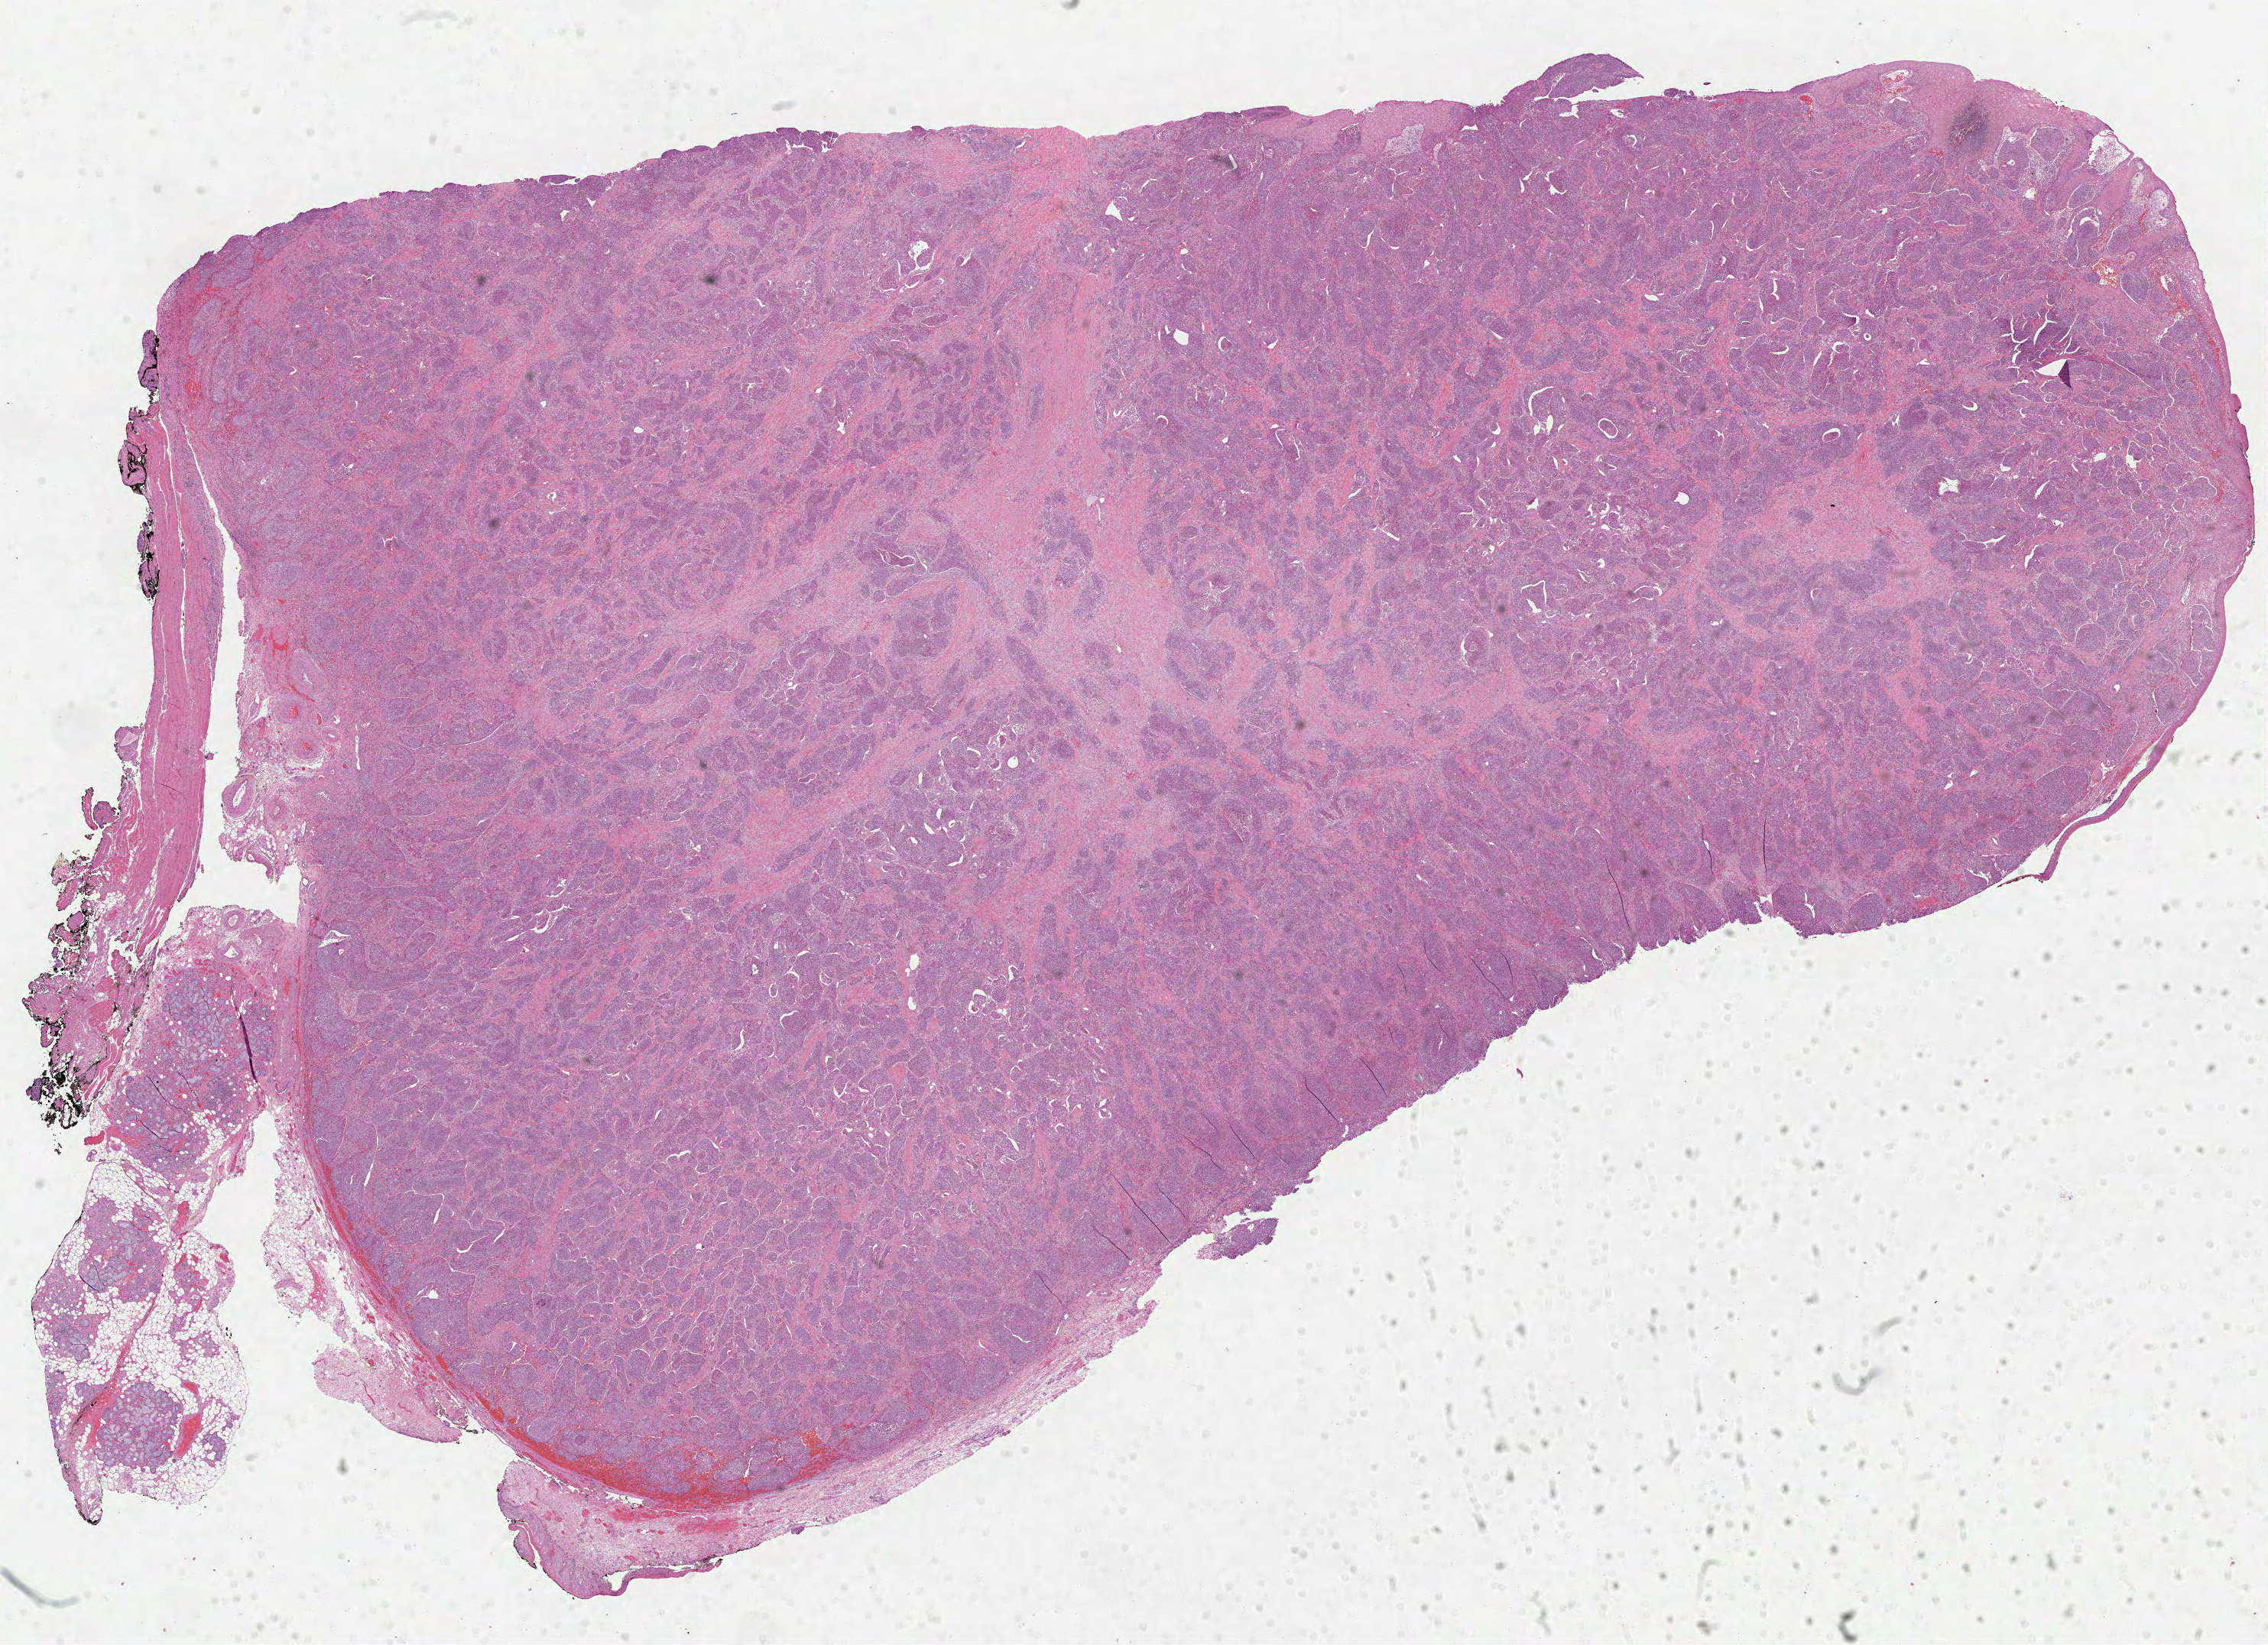
Whole-slide histology image, Hematoxylin and eosin (H&E) stained — whole scanned area (about 23.9 x 17.4 mm, slide scanned at 40x) shown as a low-resolution overview. FFPE section. Primary tumour sample from the head and neck. Patient: male, age at initial diagnosis 69 years. Histologic grade: G1 (well differentiated).
AJCC pathologic stage: IVA (7th edition). Histologic diagnosis: Squamous cell carcinoma, NOS (oropharynx, NOS).